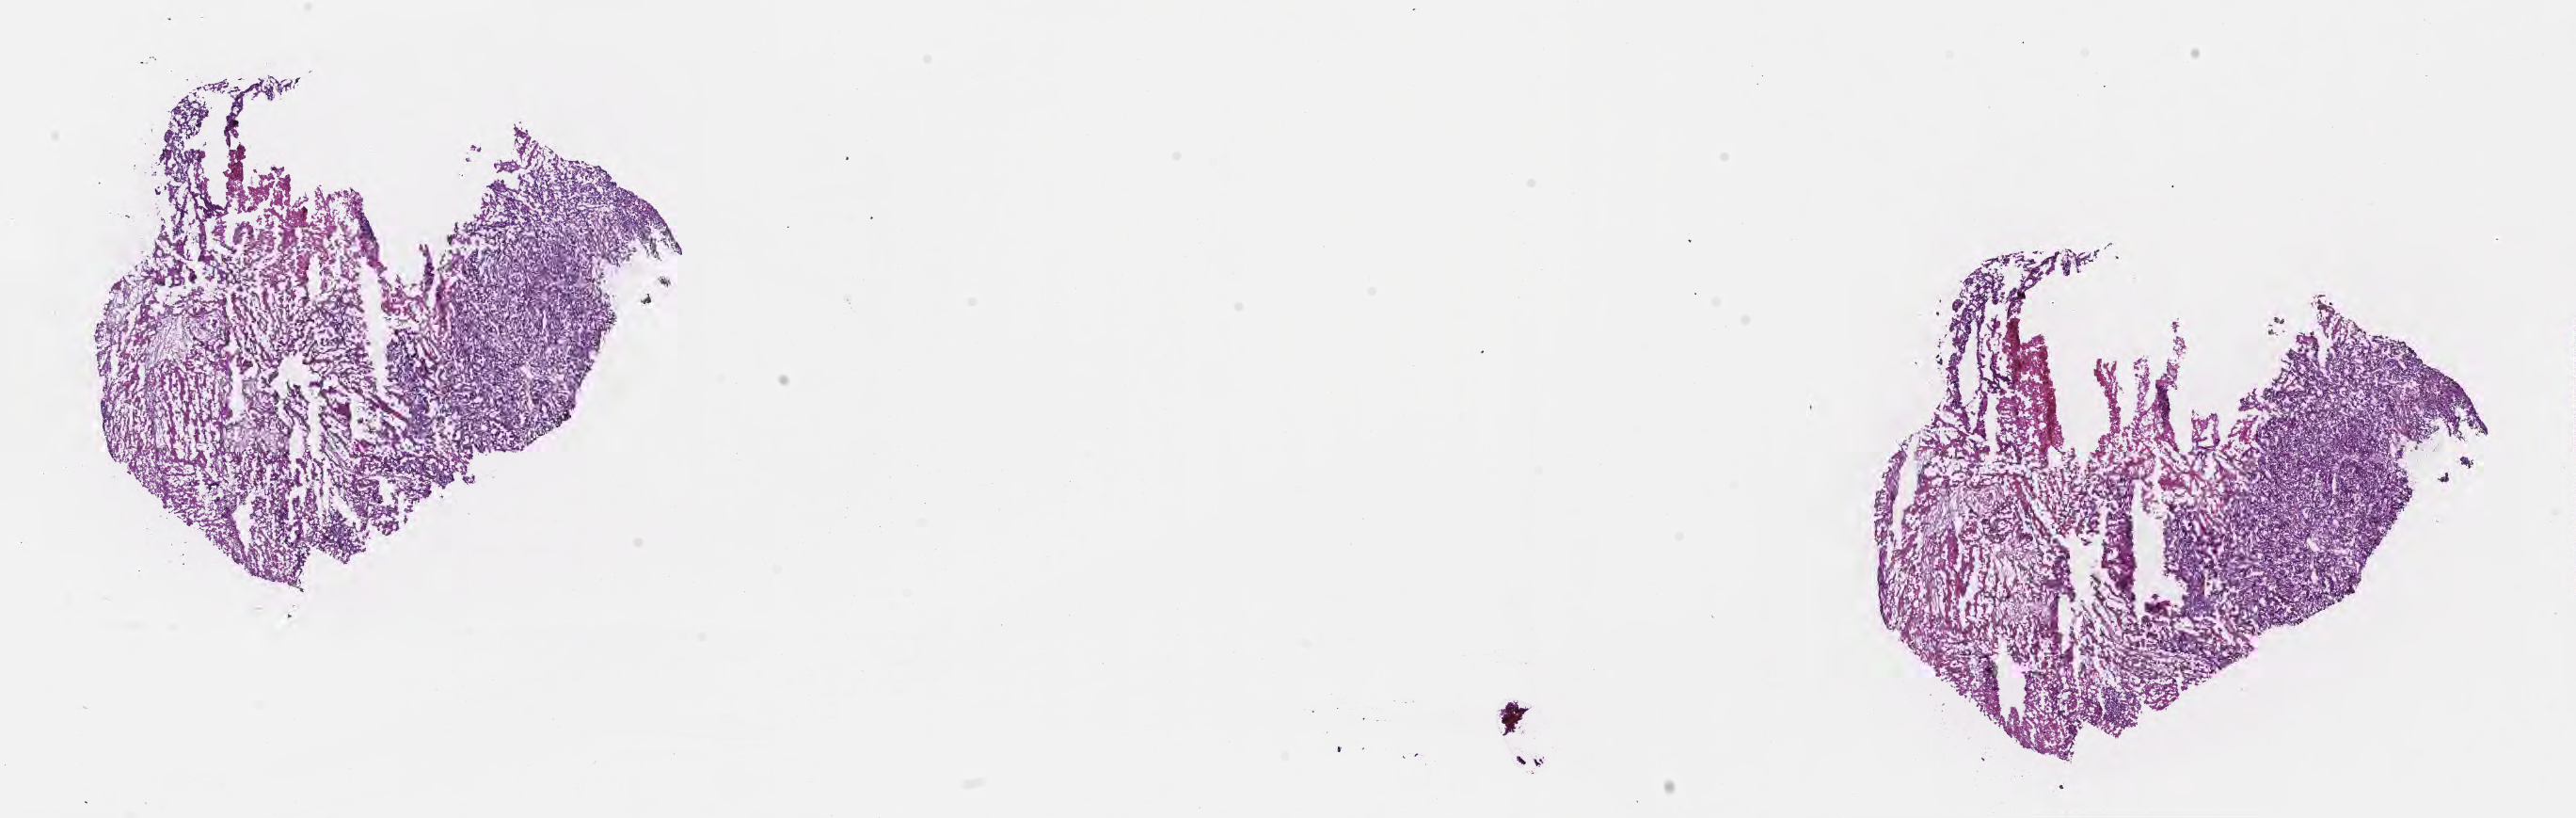
Hematoxylin and eosin (H&E) whole-slide image, low-resolution overview of the scanned area, about 22.1 x 7.0 mm, frozen section, specimen: metastatic tumor tissue, resected from brain. Patient: female, age at initial diagnosis 47 years. Slide review estimates, as recorded: tumor cells 35%, tumor nuclei 35%, stromal cells 55%, necrosis 5%, normal cells 5%. Infiltration values recorded for this section: lymphocyte infiltration 5%, monocyte infiltration 0%, neutrophil infiltration 0%.
Patient diagnosis (primary): Adenocarcinoma, NOS. Section: top of the tissue portion.